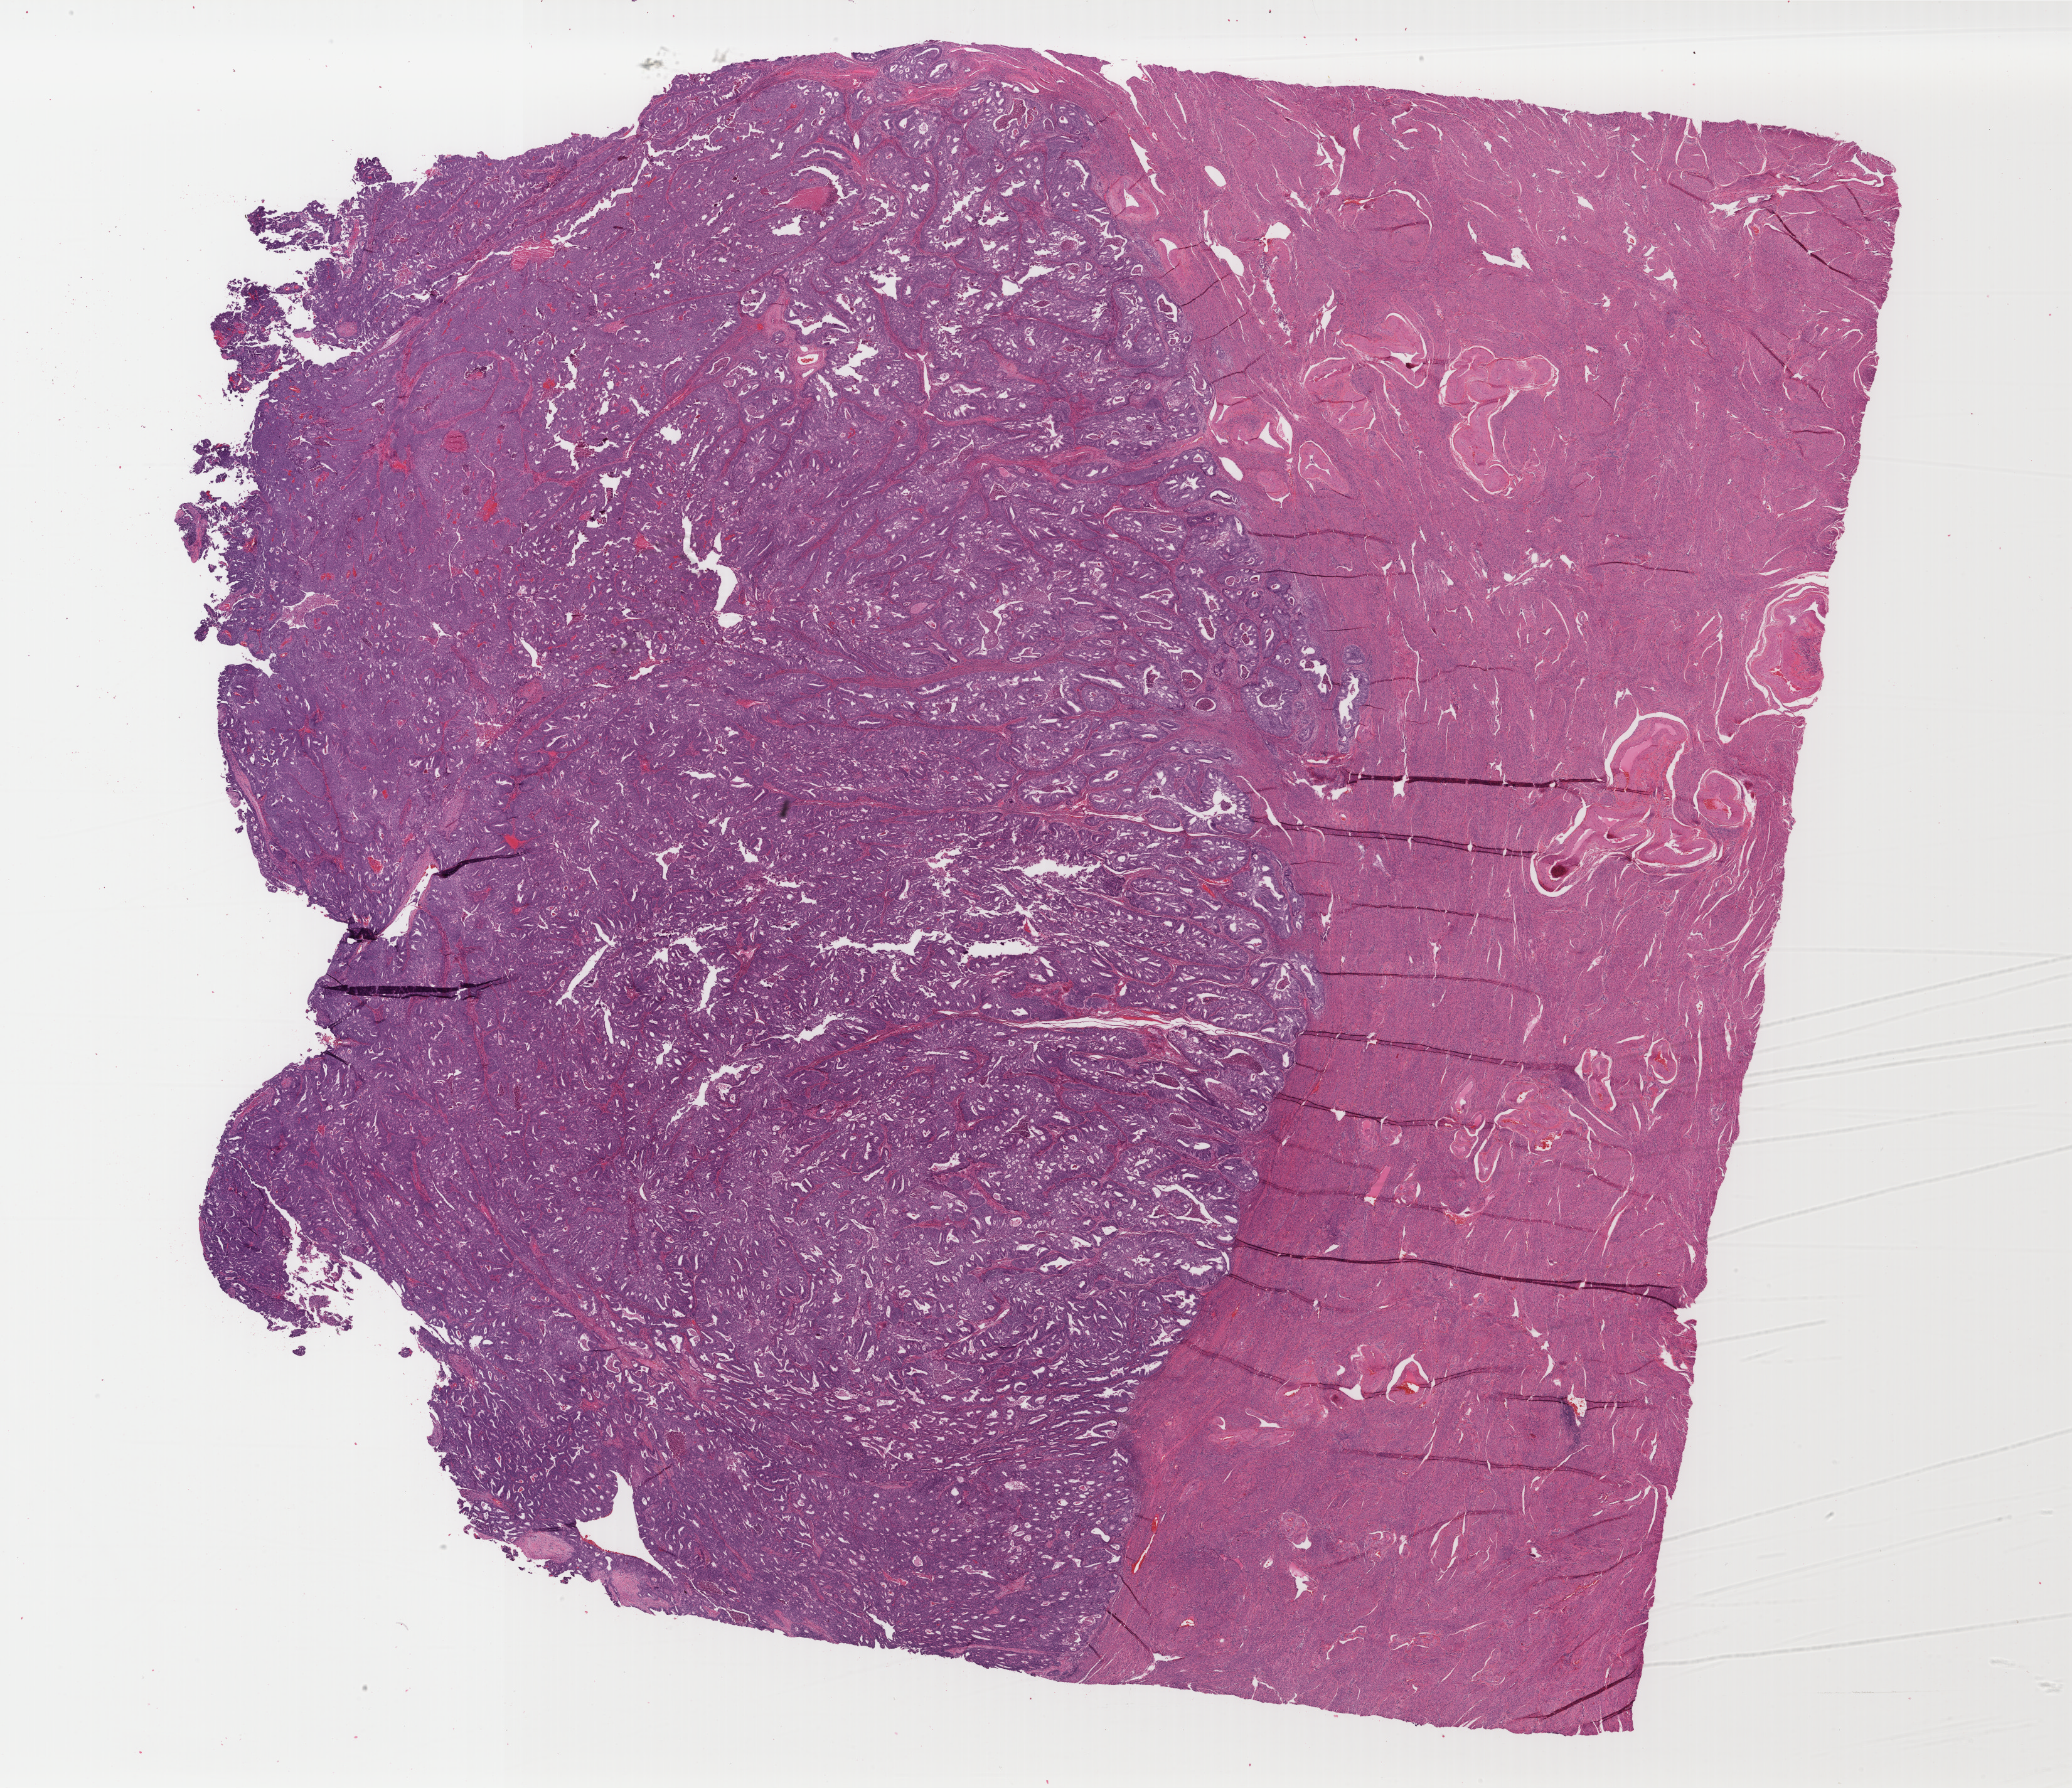
Whole-slide histology image, Hematoxylin and eosin (H&E) stained, a low-resolution overview of the entire scanned area, about 26.2 x 22.6 mm; formalin-fixed paraffin-embedded (FFPE) diagnostic section; sample: primary tumour, uterus. Female patient; age at initial diagnosis 58 years. Histologic grade: G2 (moderately differentiated).
FIGO stage: IB. Diagnosis: Endometrioid adenocarcinoma, NOS (endometrium).